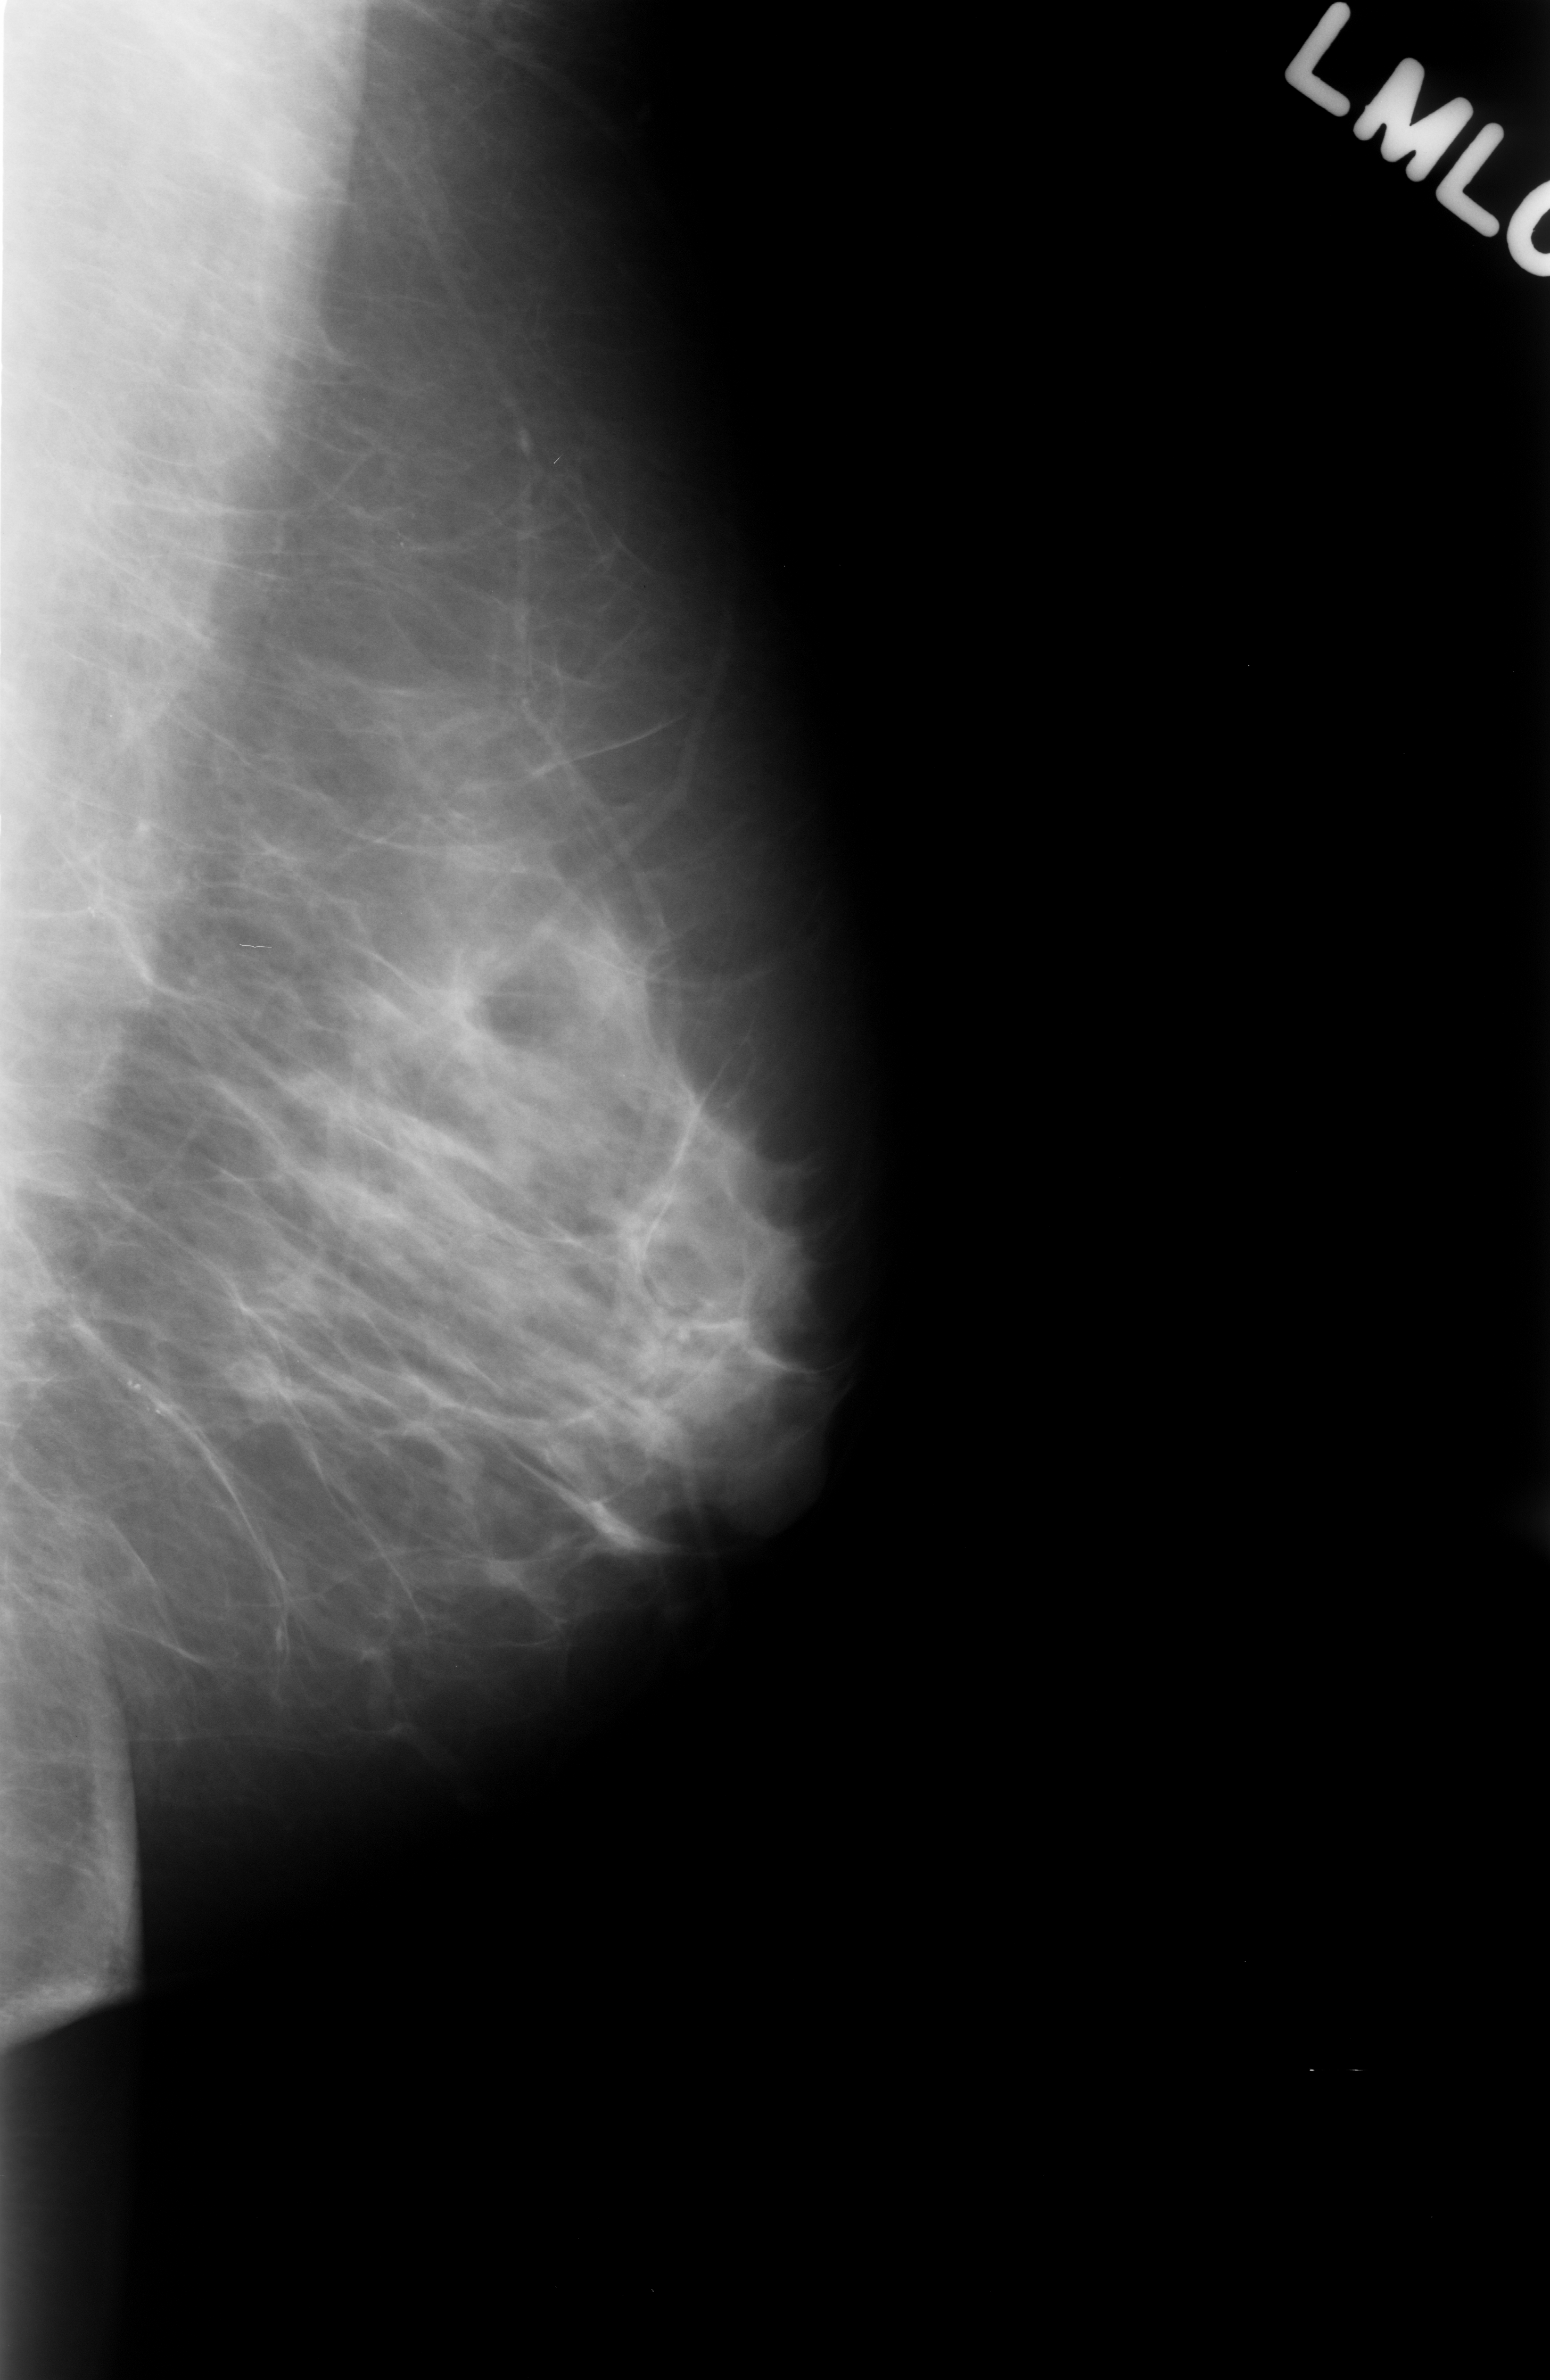
Scanned film-screen mammogram, left breast, MLO view.
- Radiologist-marked abnormalities on this image: calcifications, morphology punctate, distribution clustered; BI-RADS assessment category 4; subtlety rating 4 on a 1 (subtle) to 5 (obvious) scale; pathology (as recorded): benign.